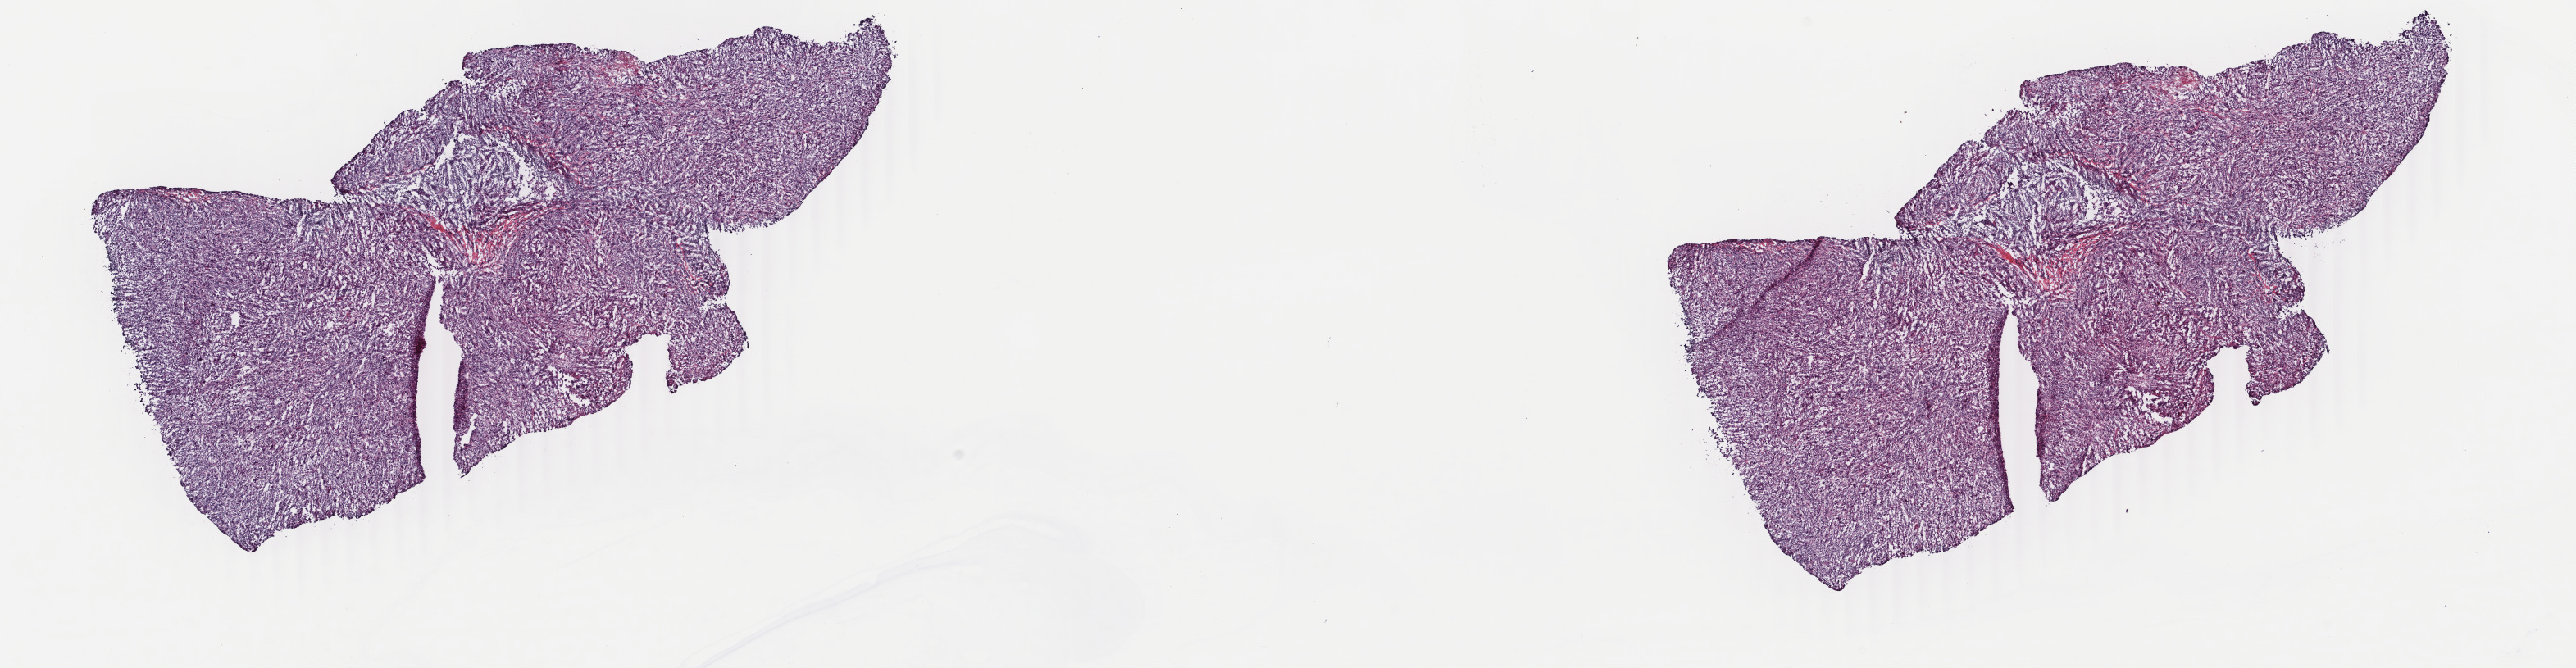
H&E-stained whole-slide image — a low-resolution overview of the entire scanned area, about 25.0 x 6.5 mm (from a 40x scan); frozen section from the top of the tissue portion; metastatic tumour sample, sampled site: parotid gland. Male patient; age at initial diagnosis 78 years.
This section: metastatic tumour tissue. Patient diagnosis: Malignant melanoma, NOS.